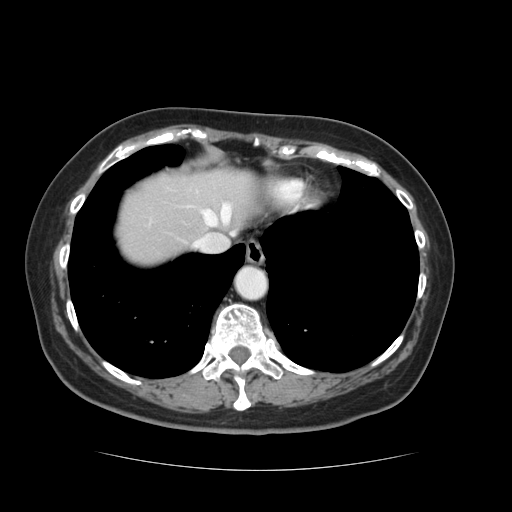
Contrast-enhanced abdominal CT, one axial slice. Position 112 of 128 along the scan axis. 120 kVp. Intravenous contrast given. Soft-tissue window (W 400 / L 40 HU). 2.5 mm slice thickness. 512 × 512 image matrix, field of view 366 × 366 mm. Female patient, age 67 years. Case-level facts recorded for this patient, not image findings: diagnosis: colorectal cancer liver metastases, imaged before liver resection; multiple liver metastases: yes; largest metastasis: 3 cm; chemotherapy before resection: no.
Structures marked on this image (expert manual segmentation):
- hepatic veins: bounding box <193,203,234,251> (left, top, right, bottom; pixels)
- liver: <117,167,255,264>
- planned liver remnant (the part of the liver to remain after resection): <117,169,255,265>